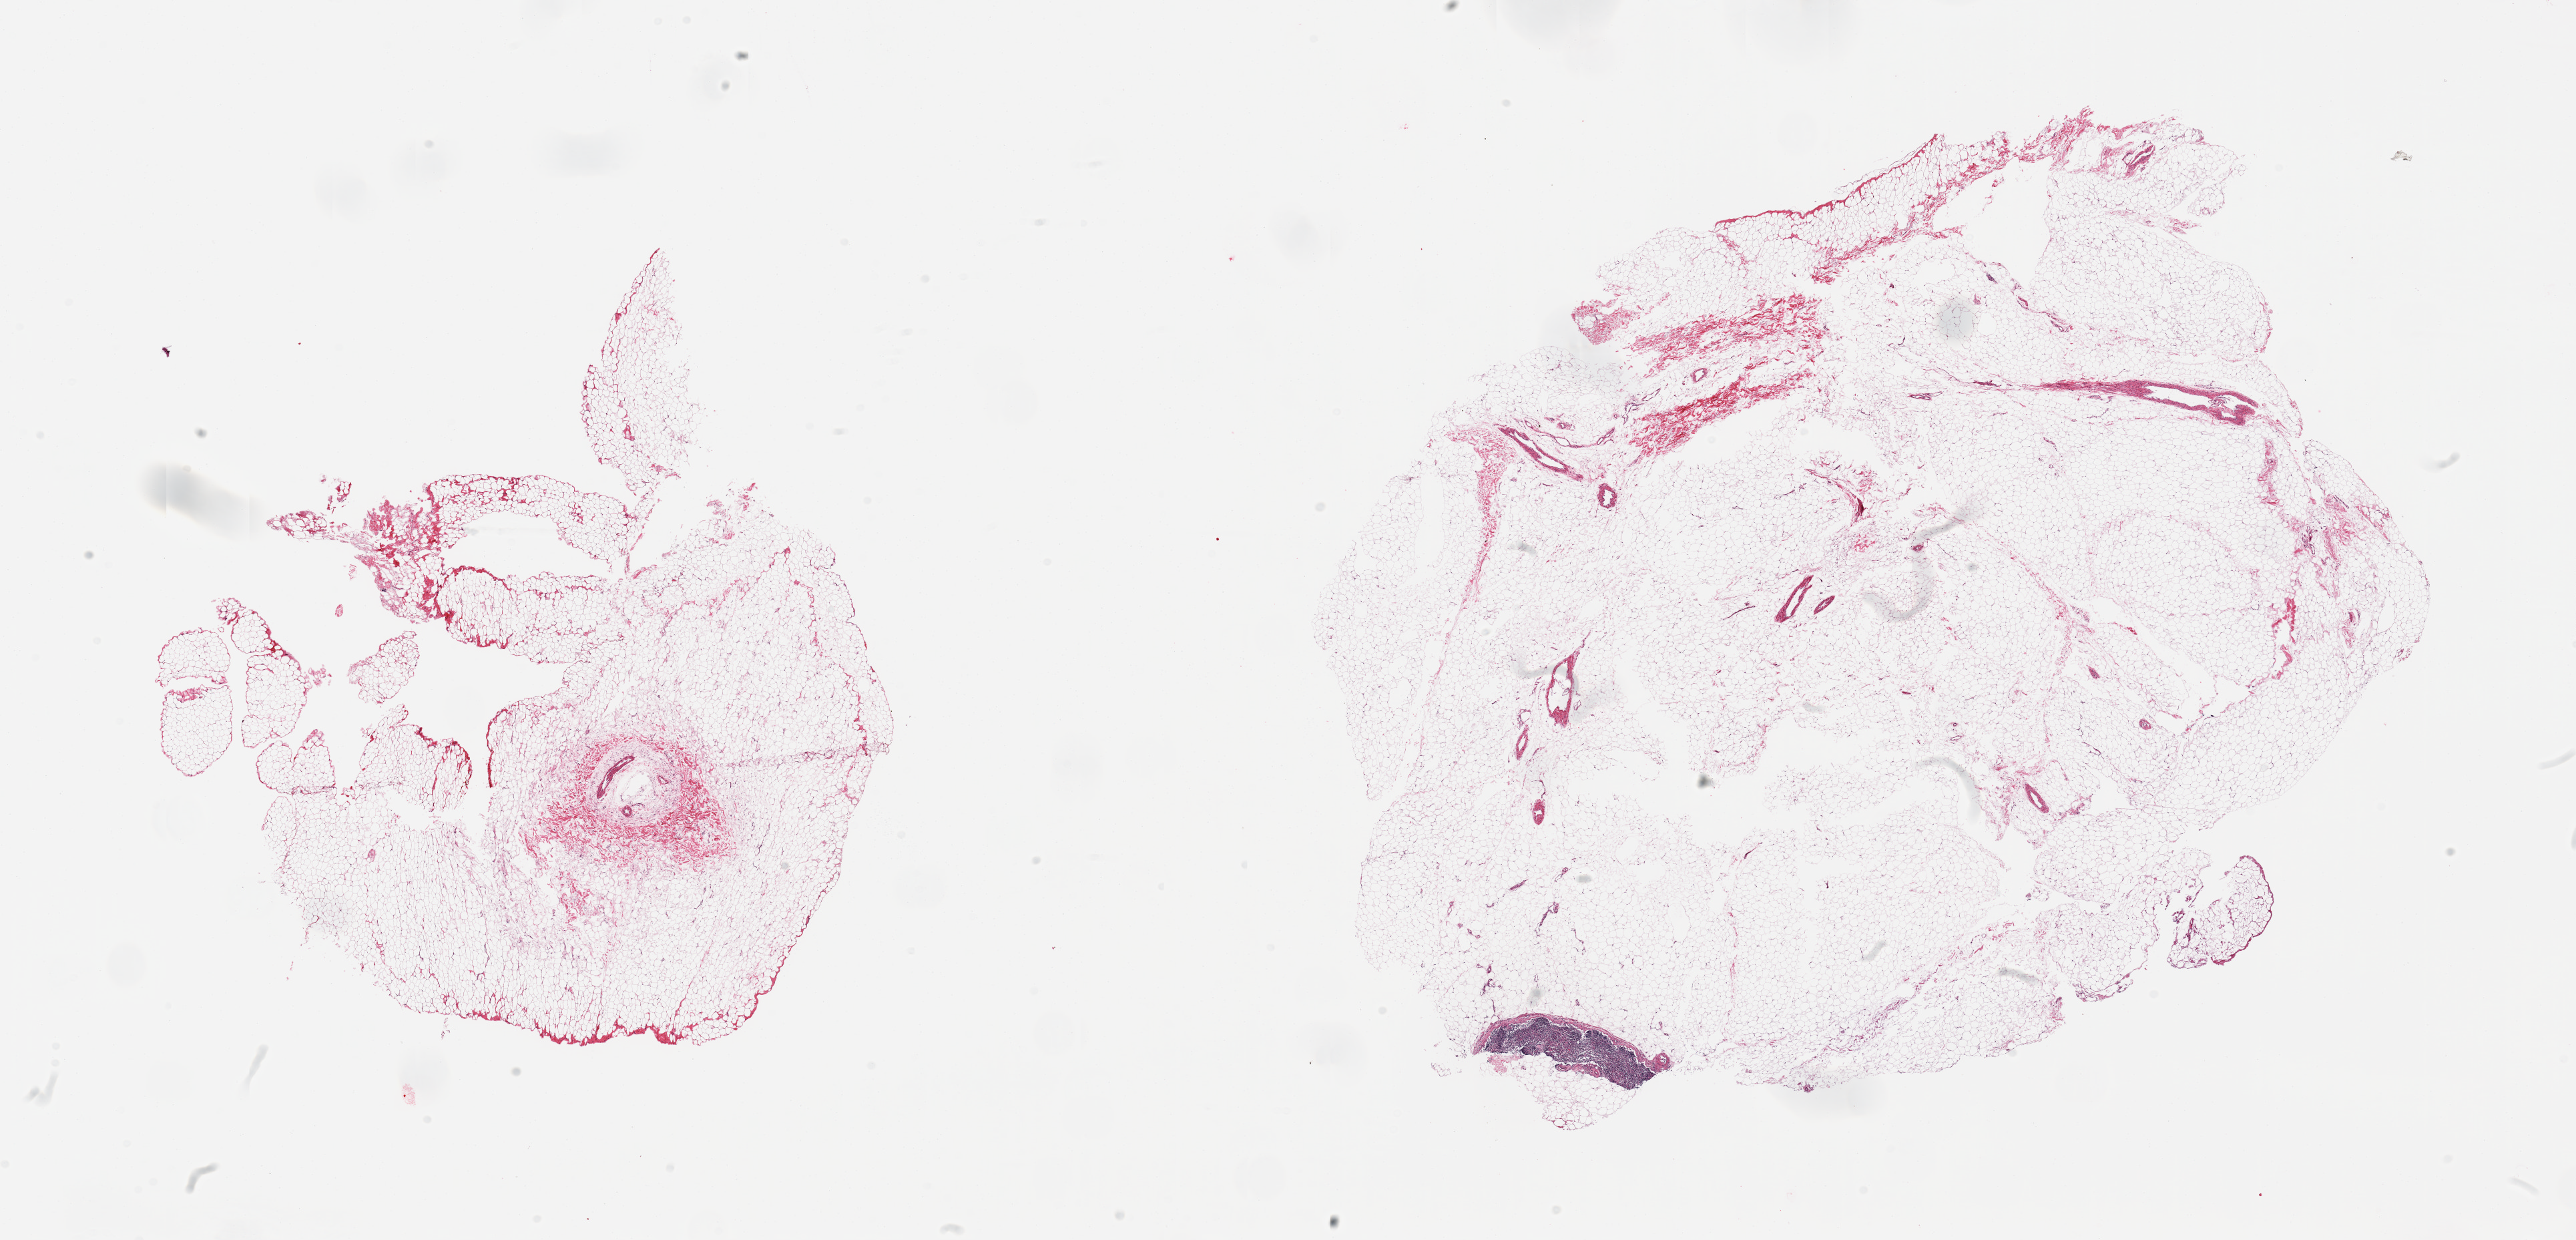
H&E whole-slide image — a low-resolution overview of the entire scanned area, about 30.5 x 14.7 mm, PAXgene-fixed paraffin-embedded (PFPE) section, sampled site (target tissue): omentum, donor tissue sample. Donor sex: male.
Pathologist's review note for this sample: 2 pieces; 2mm partial lymph node in 1 piece.